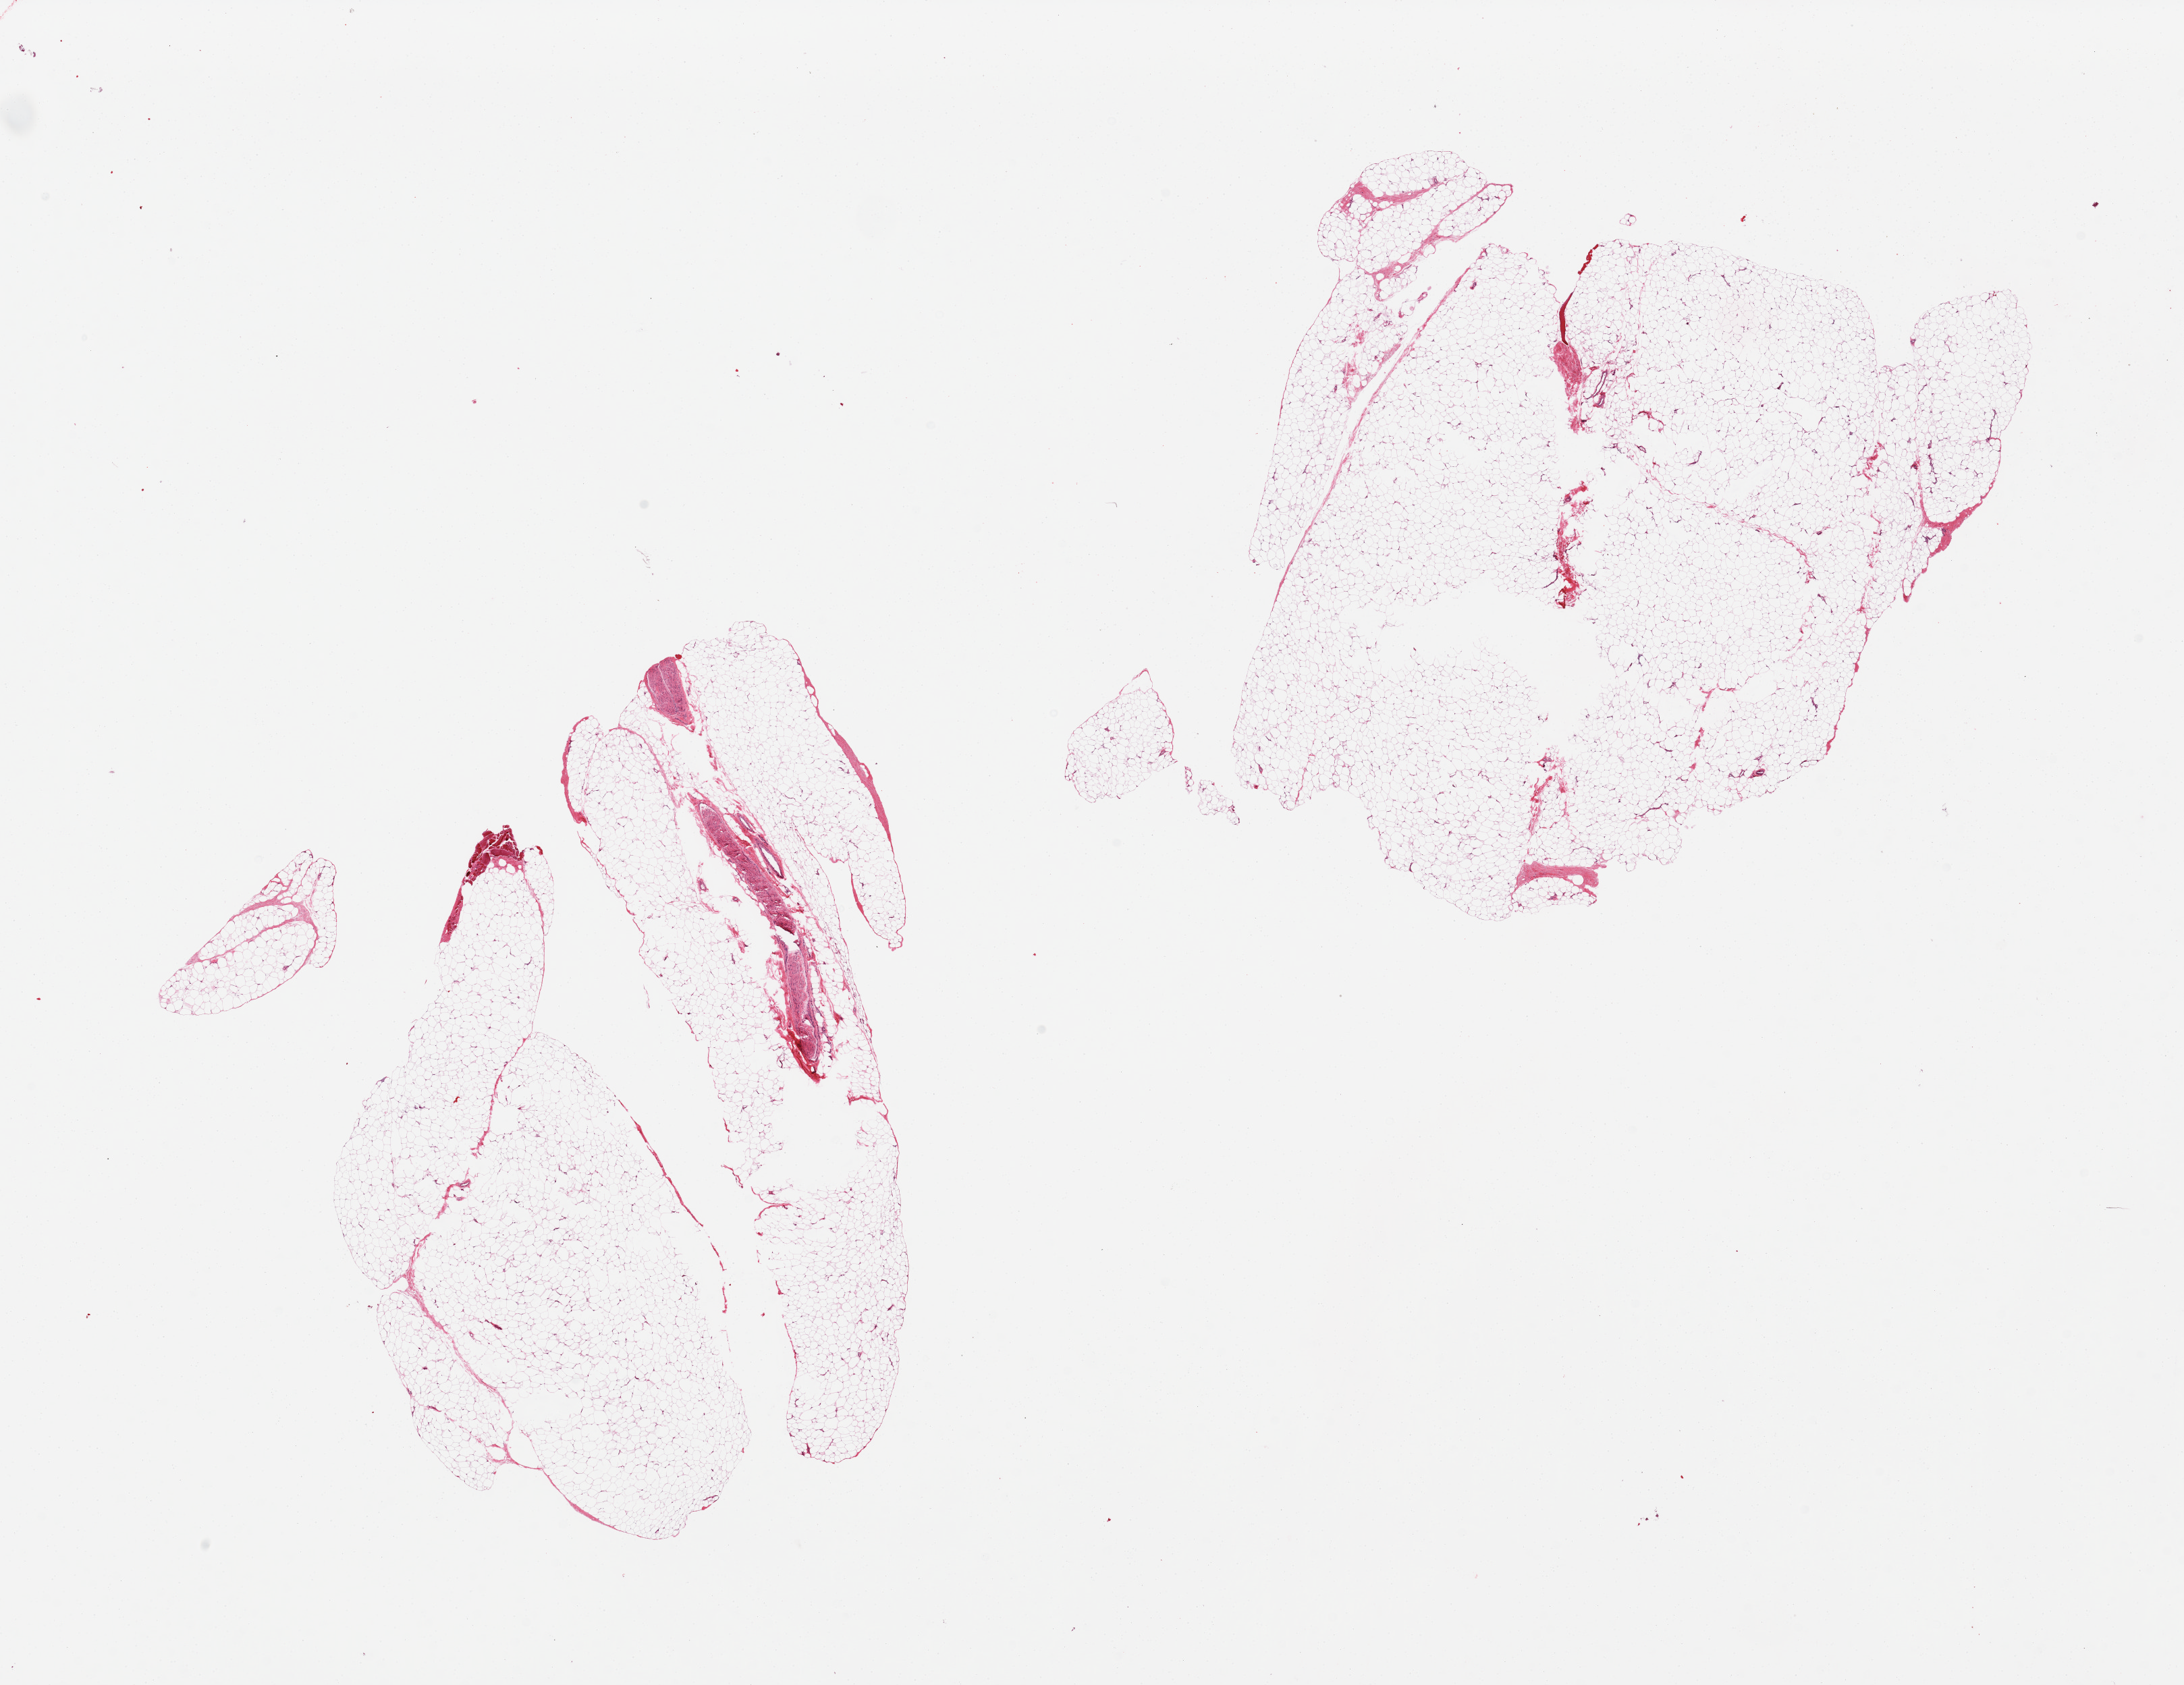
Digitized haematoxylin and eosin-stained section, brightfield — low-resolution overview of the scanned area, about 25.6 x 19.7 mm; PAXgene-fixed, paraffin-embedded tissue; section of adipose tissue (target tissue); donor tissue sample. Donor: male.
Review note (as recorded): 2 pieces, includes portion of nerve and small fragment of skeletal muscle.